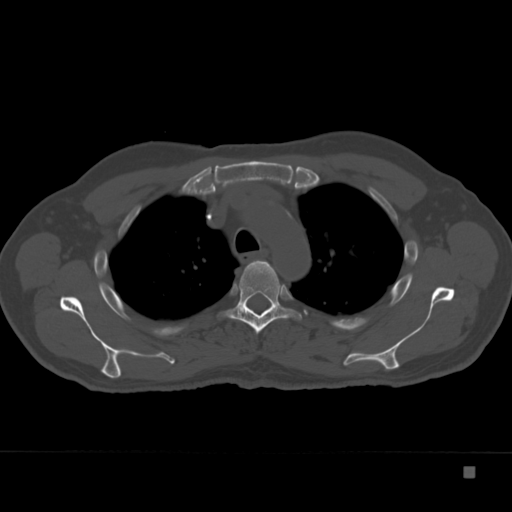
CT including the spine, one axial slice. Position 273 of 332 along the scan axis. Bone window (W 1800 / L 400 HU). 1.5 mm slice thickness. 512 × 512 image matrix, field of view 389 × 389 mm. Male patient, age 72 years. Case-level facts recorded for this patient, not image findings: primary cancer: skeletal.
Structures marked on this image (semi-automatic segmentation, software-assisted and operator-edited):
- T4 vertebra: bounding box [x1, y1, x2, y2] px = [224, 260, 302, 334]